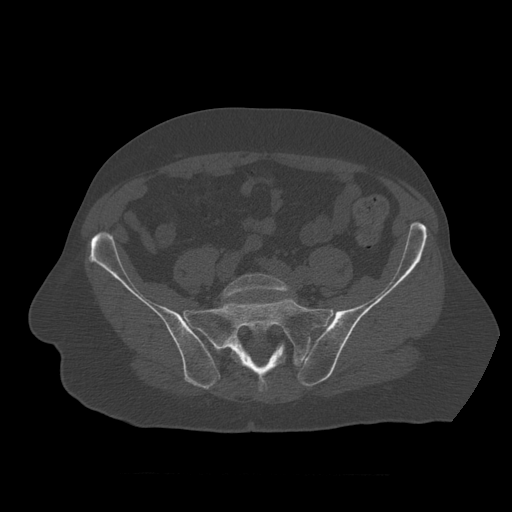
CT including the spine, one axial slice. Slice 237 of 450 in the series (ordered by position). Reconstruction kernel STANDARD. Bone window (W 1800 / L 400 HU). 512 × 512 image matrix, field of view 405 × 405 mm. Patient age 75 years. From the clinical record (not read from this slice): primary cancer: prostate.
Structures marked on this image (semi-automatic segmentation, software-assisted and operator-edited):
- L5 vertebra: bounding box <222,274,292,300> (left, top, right, bottom; pixels)